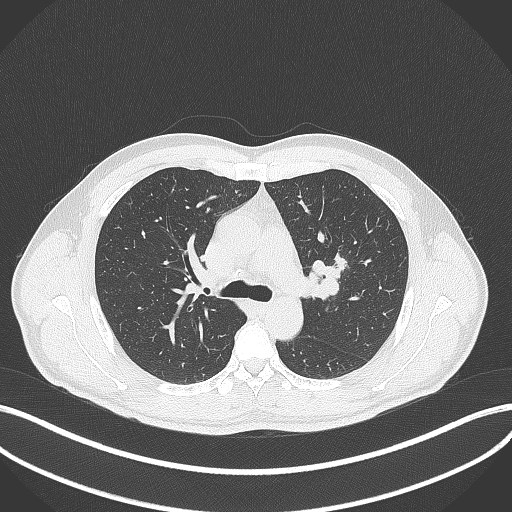
Chest CT, one axial slice. Position 277 of 392 along the scan axis. Reconstruction kernel B70f. Lung window (W 1500 / L -600 HU). 1 mm slice thickness. 512 × 512 image matrix. Male patient, age 50 years. Case-level facts recorded for this patient, not image findings: clinical TNM (as recorded): T1c N1 M1b.
Structures marked on this image (rectangle marked by the reading radiologist):
- lung tumour (recorded histology: squamous cell carcinoma): bounding box [x1, y1, x2, y2] px = [308, 256, 351, 301]